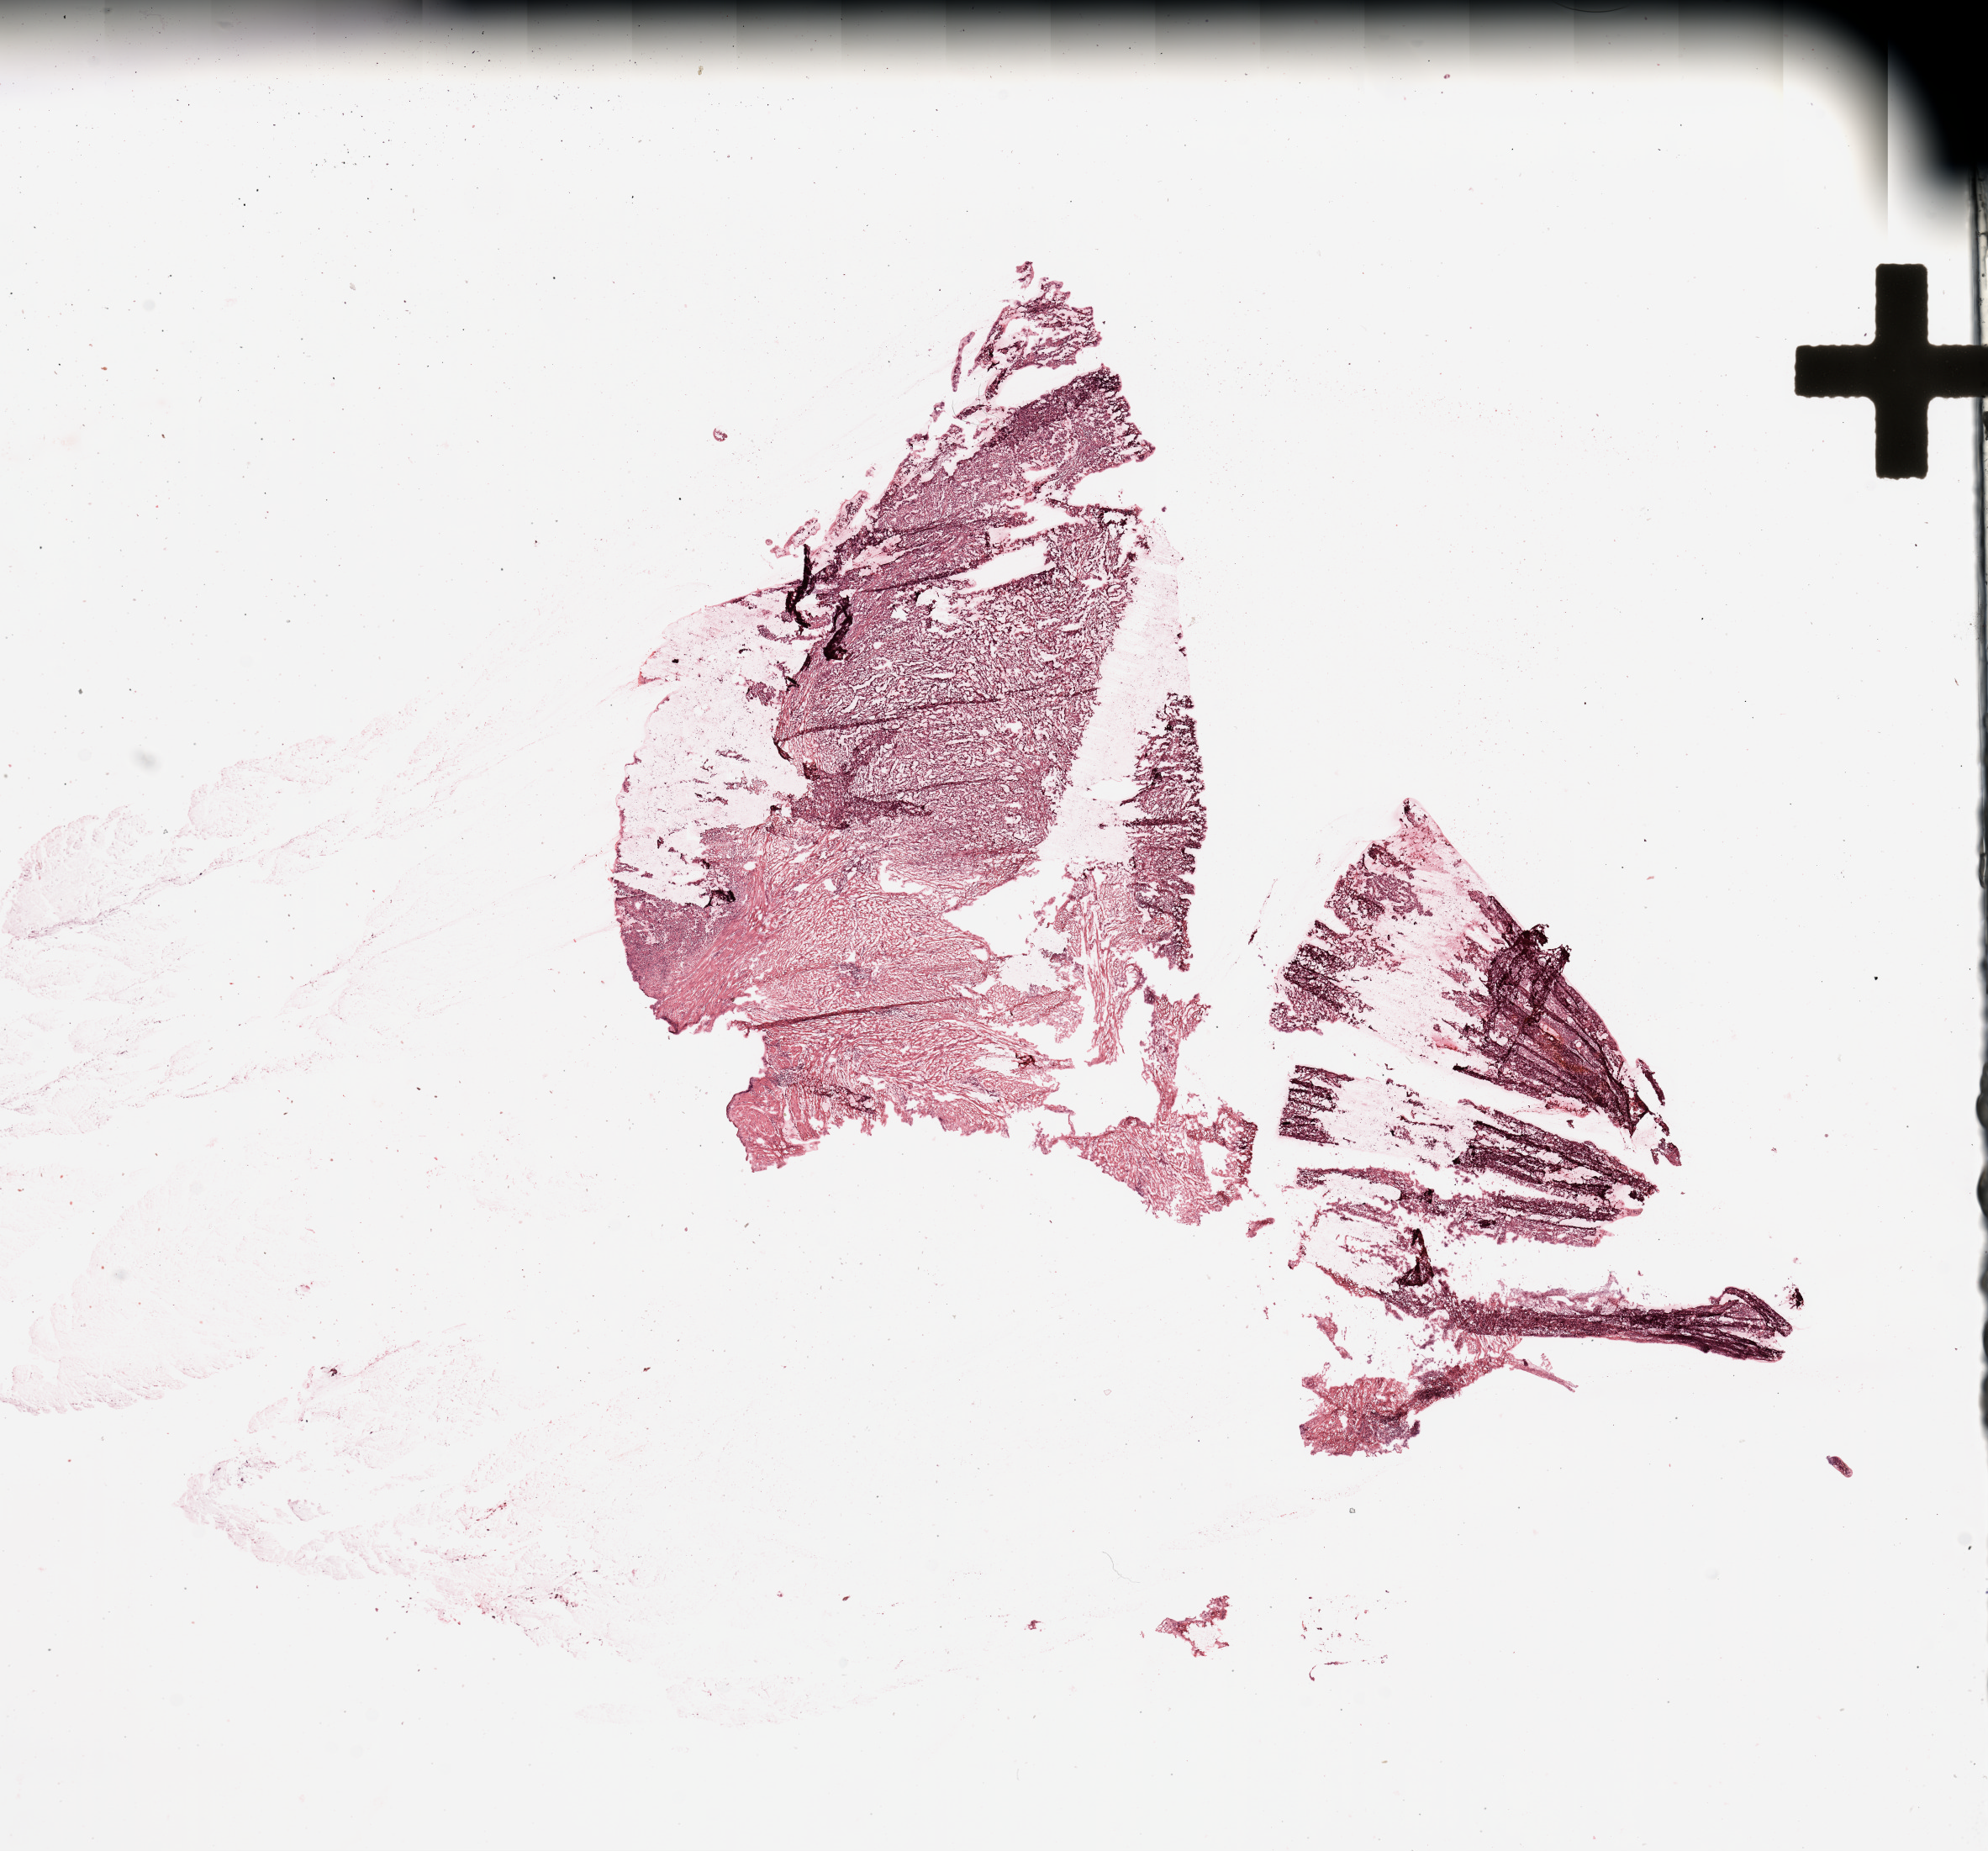
H&E-stained whole-slide image — whole scanned area (about 18.7 x 17.4 mm, acquisition: 20x scan) shown as a low-resolution overview, tumour tissue sample, uterus. Patient: female, age 57 years. Histologic grade: G3 (poorly differentiated).
AJCC pathologic stage: I. Diagnosis: Endometrioid adenocarcinoma, NOS.